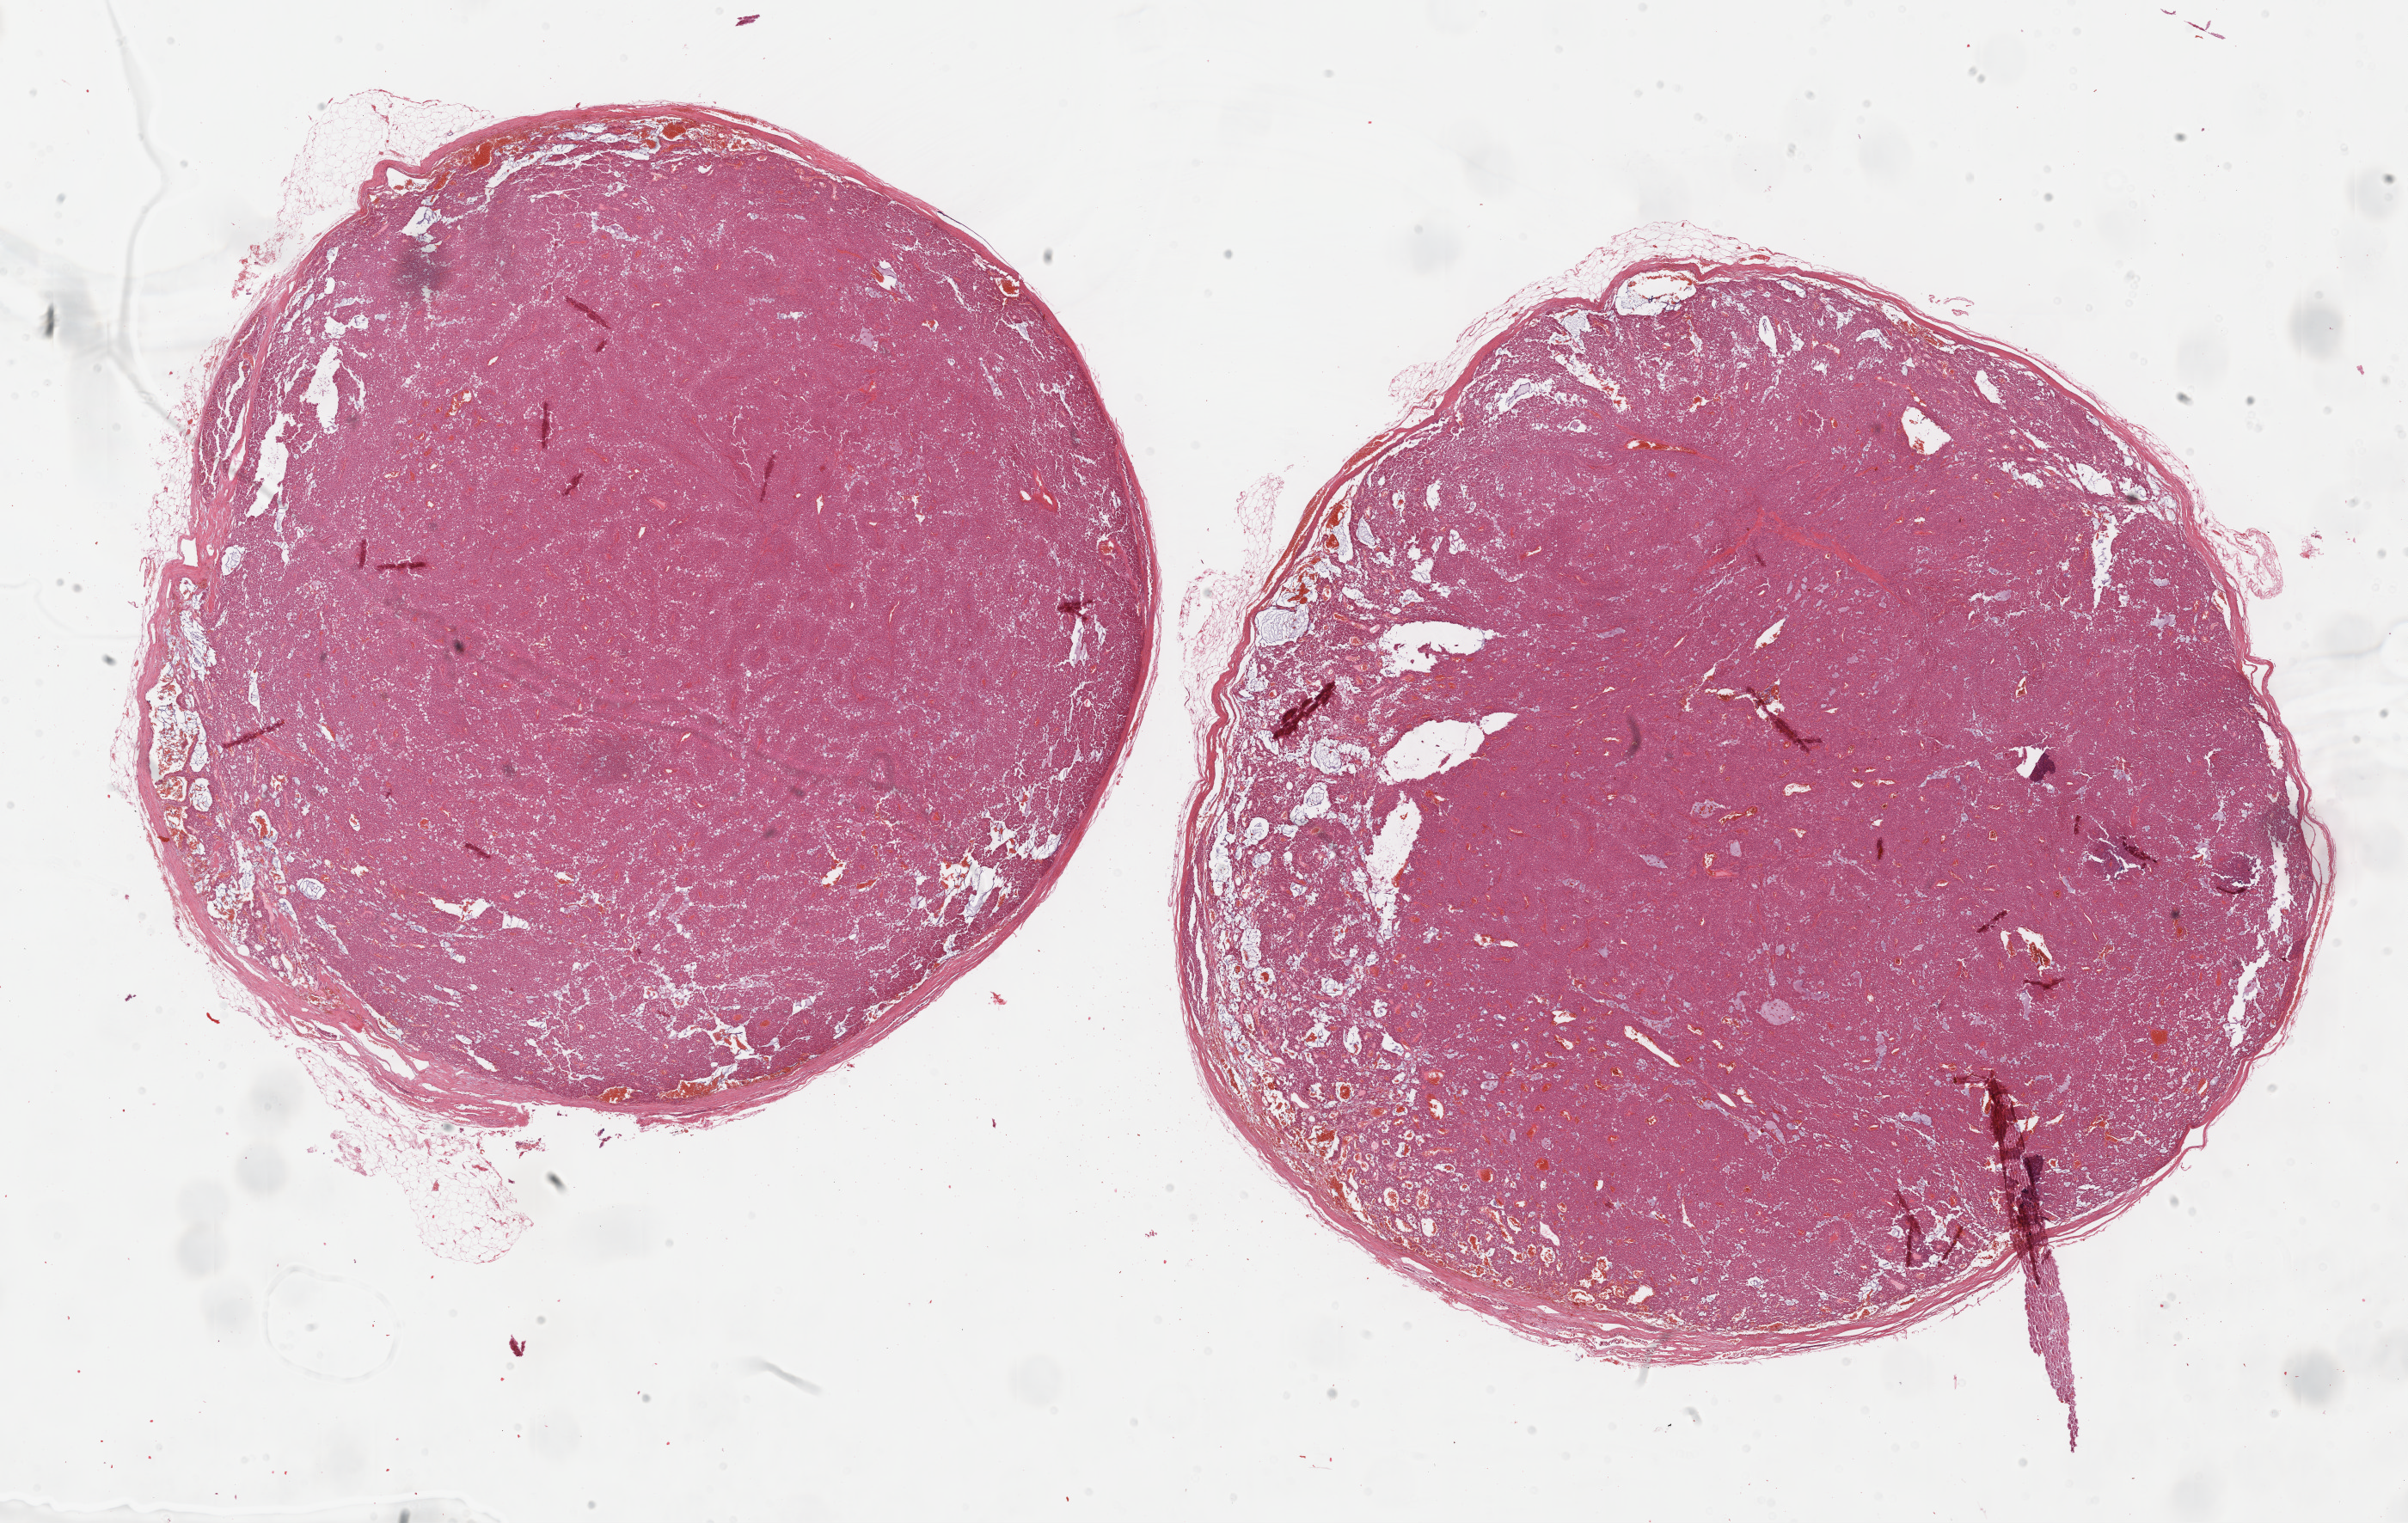
Whole-slide histology image, H&E-stained, shown as a low-resolution overview of the whole scanned area (about 22.7 x 14.3 mm, from a 40x scan); formalin-fixed paraffin-embedded (FFPE) diagnostic section; sample: primary tumour, adrenal cortex. Male, age 61 years at initial diagnosis.
Lymph nodes positive (case pathology): 6 of 8 examined. Pathologic diagnosis: Adrenal cortical carcinoma (cortex of adrenal gland).